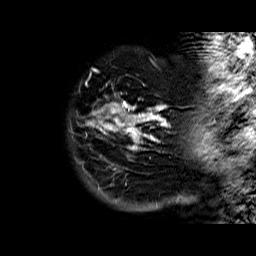
Breast MRI (dynamic contrast-enhanced), one sagittal slice. Dynamic contrast-enhanced series, time point 2 of 6 at this slice position (early post-contrast). 1.5 T. TE 6.3 ms, TR 32.4 ms. 4 mm slice thickness. 256 × 256 image matrix, field of view 200 × 200 mm. Female patient. Case-level facts recorded for this patient, not image findings: setting: breast cancer imaged before/during neoadjuvant chemotherapy; receptor status: HR-positive, HER2-negative.
Structures marked on this image (semi-automatically segmented with operator editing):
- analysis volume of interest (the breast-tissue region the enhancement analysis was run in; not a lesion): bounding box [x1, y1, x2, y2] px = [78, 83, 176, 183]
- tumour enhancement mask (voxels above the 100 % enhancement threshold inside the analysis volume of interest): [86, 93, 167, 150]